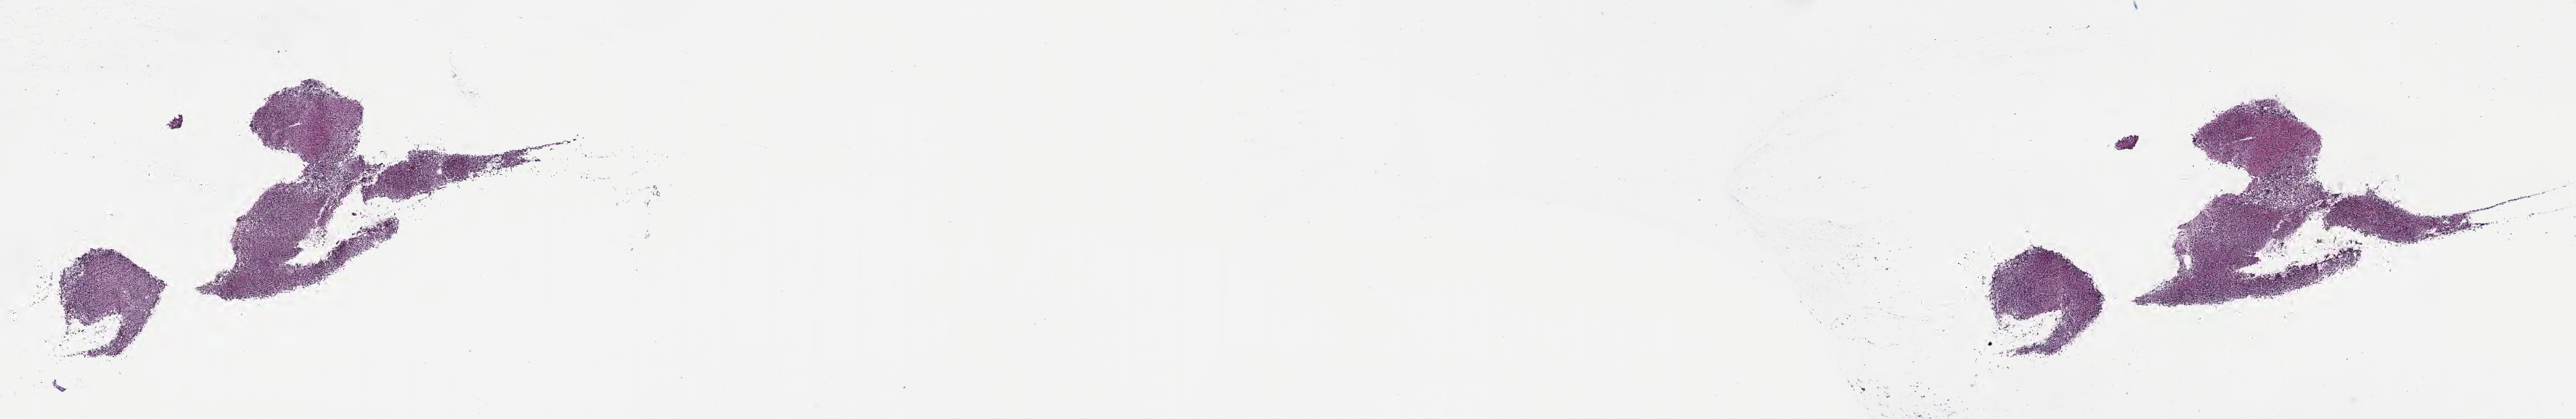
Digitized hematoxylin and eosin (H&E)-stained section of tumor tissue from the brain — a low-resolution overview of the entire scanned area, about 28.7 x 4.7 mm; frozen section. Patient: male, age 191 months (15 years 11 months).
* recorded diagnosis: Neoplasm, uncertain whether benign or malignant